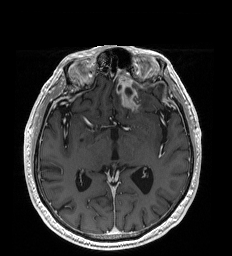
Brain MRI from a brain-tumour surgery series, one axial slice; position 109 of 192 along the scan axis; T1-weighted post-contrast; 232 × 256 image matrix. Case-level facts recorded for this patient, not image findings: histopathology: Glioblastoma; WHO grade: 4; IDH mutation: no.
Structures marked on this image (manually delineated by an expert):
- tumour: box from (x=117, y=87) to (x=138, y=111) px